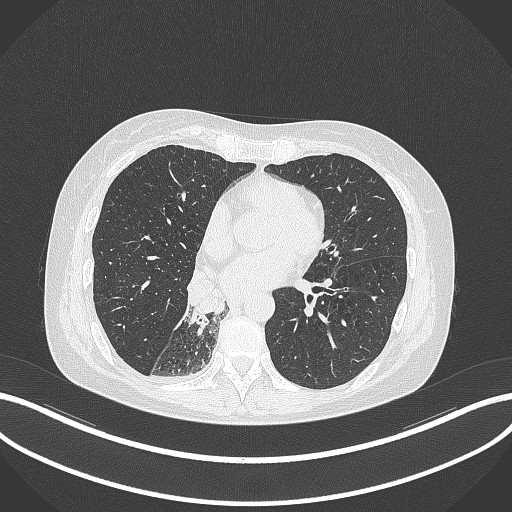
Chest CT, one axial slice. Slice 133 of 329 in the series (ordered by position). Reconstruction kernel B70f. 120 kVp. Lung window (W 1500 / L -600 HU). 1 mm slice thickness. 512 × 512 image matrix, field of view 400 × 400 mm. Female patient, age 63 years. Case-level facts recorded for this patient, not image findings: clinical TNM (as recorded): T1c N0 M0.
Structures marked on this image (rectangle marked by the reading radiologist):
- lung tumour (recorded histology: adenocarcinoma): bounding box [x1, y1, x2, y2] px = [184, 271, 229, 328]